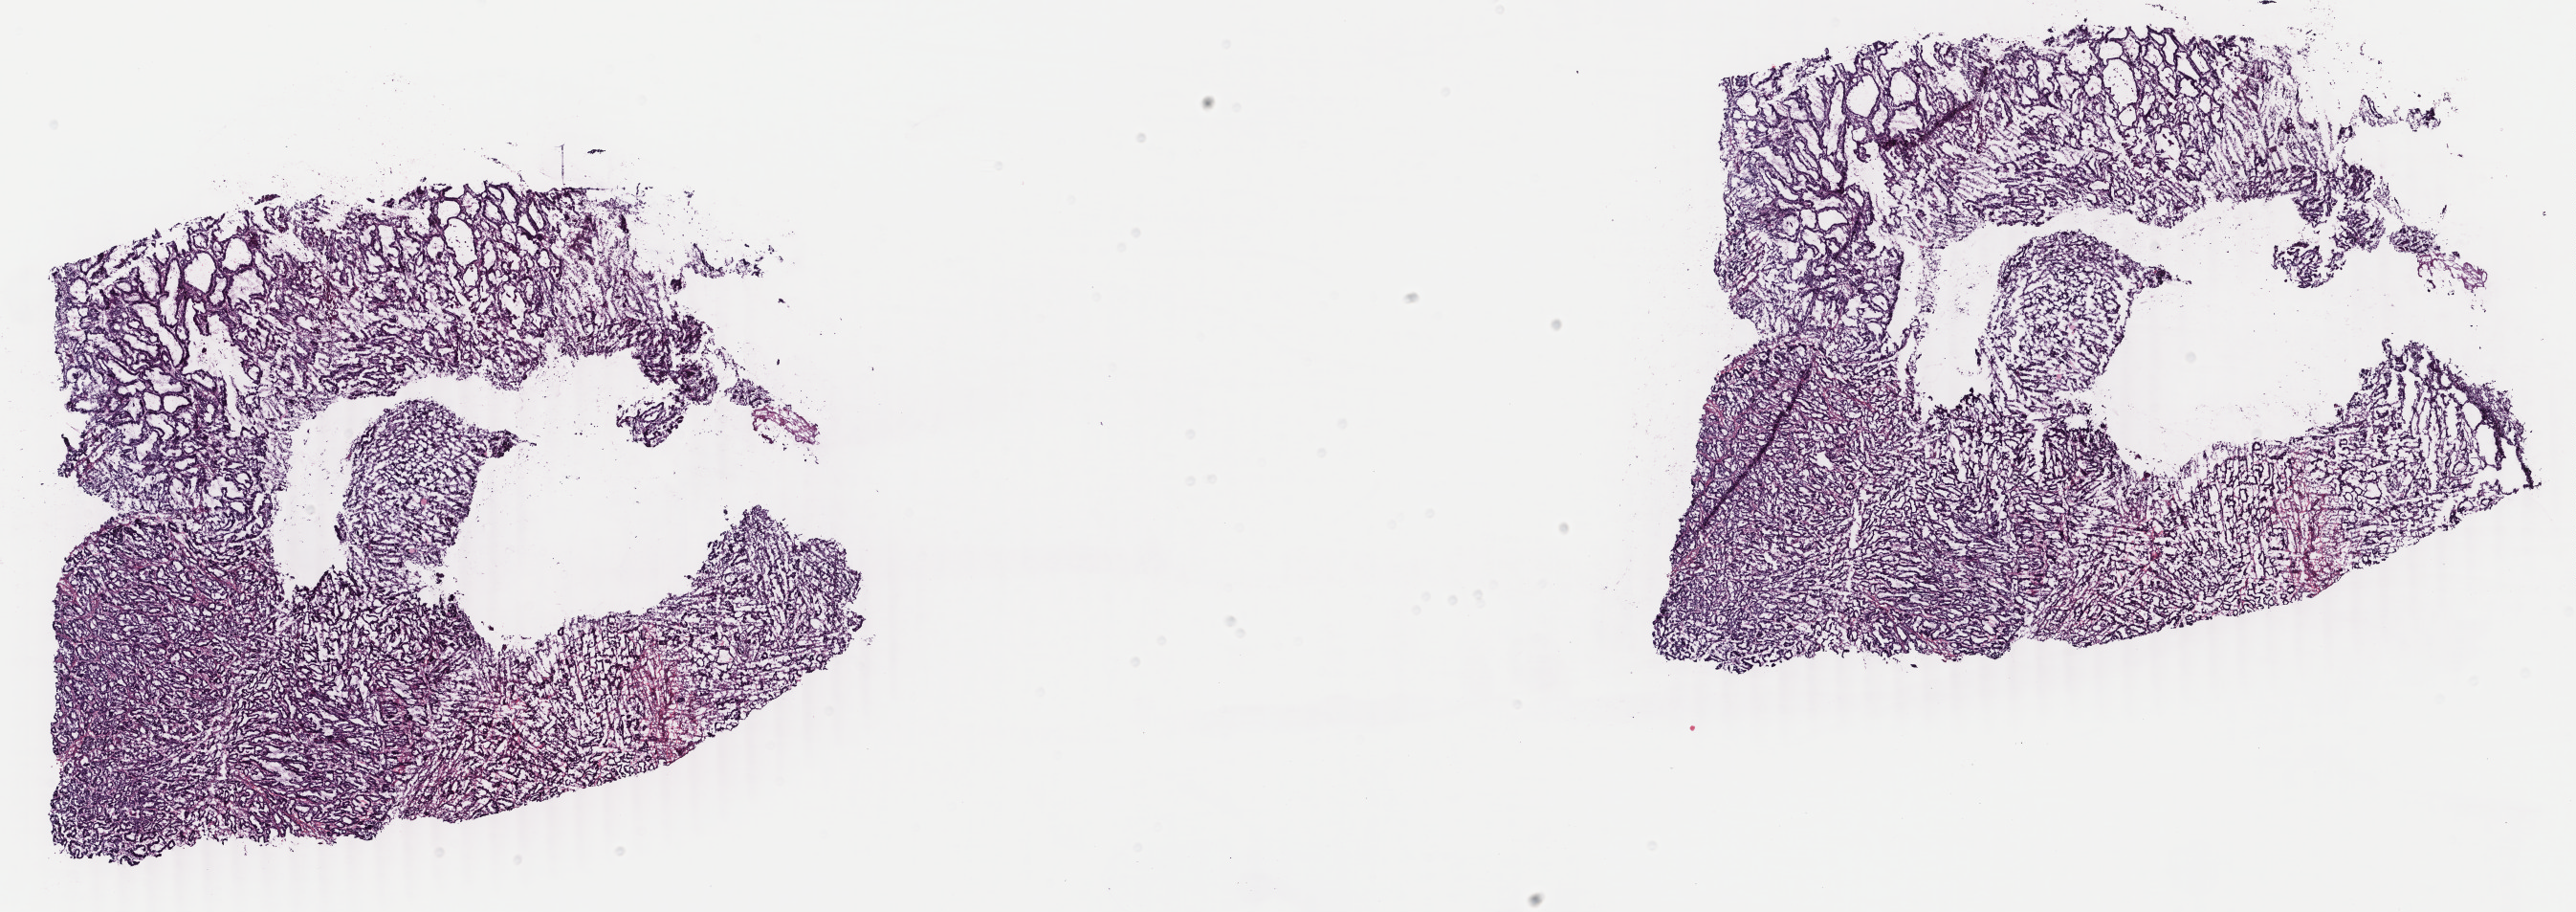
Whole-slide histology image, H&E-stained — shown as a low-resolution overview of the whole scanned area (about 21.4 x 7.6 mm), frozen section, primary tumour sample from the uterus. Patient: female, age at initial diagnosis 58 years. Histologic grade: G1 (well differentiated). Pathologist review of this section (percent, as recorded): tumour cells 100%, tumour nuclei 90%, normal cells 0%, stromal cells 0%, necrosis 0%. Infiltration values recorded for this section: lymphocyte infiltration 0%, monocyte infiltration 0%, neutrophil infiltration 0%.
FIGO stage: IA. Histologic diagnosis: Endometrioid adenocarcinoma, NOS.